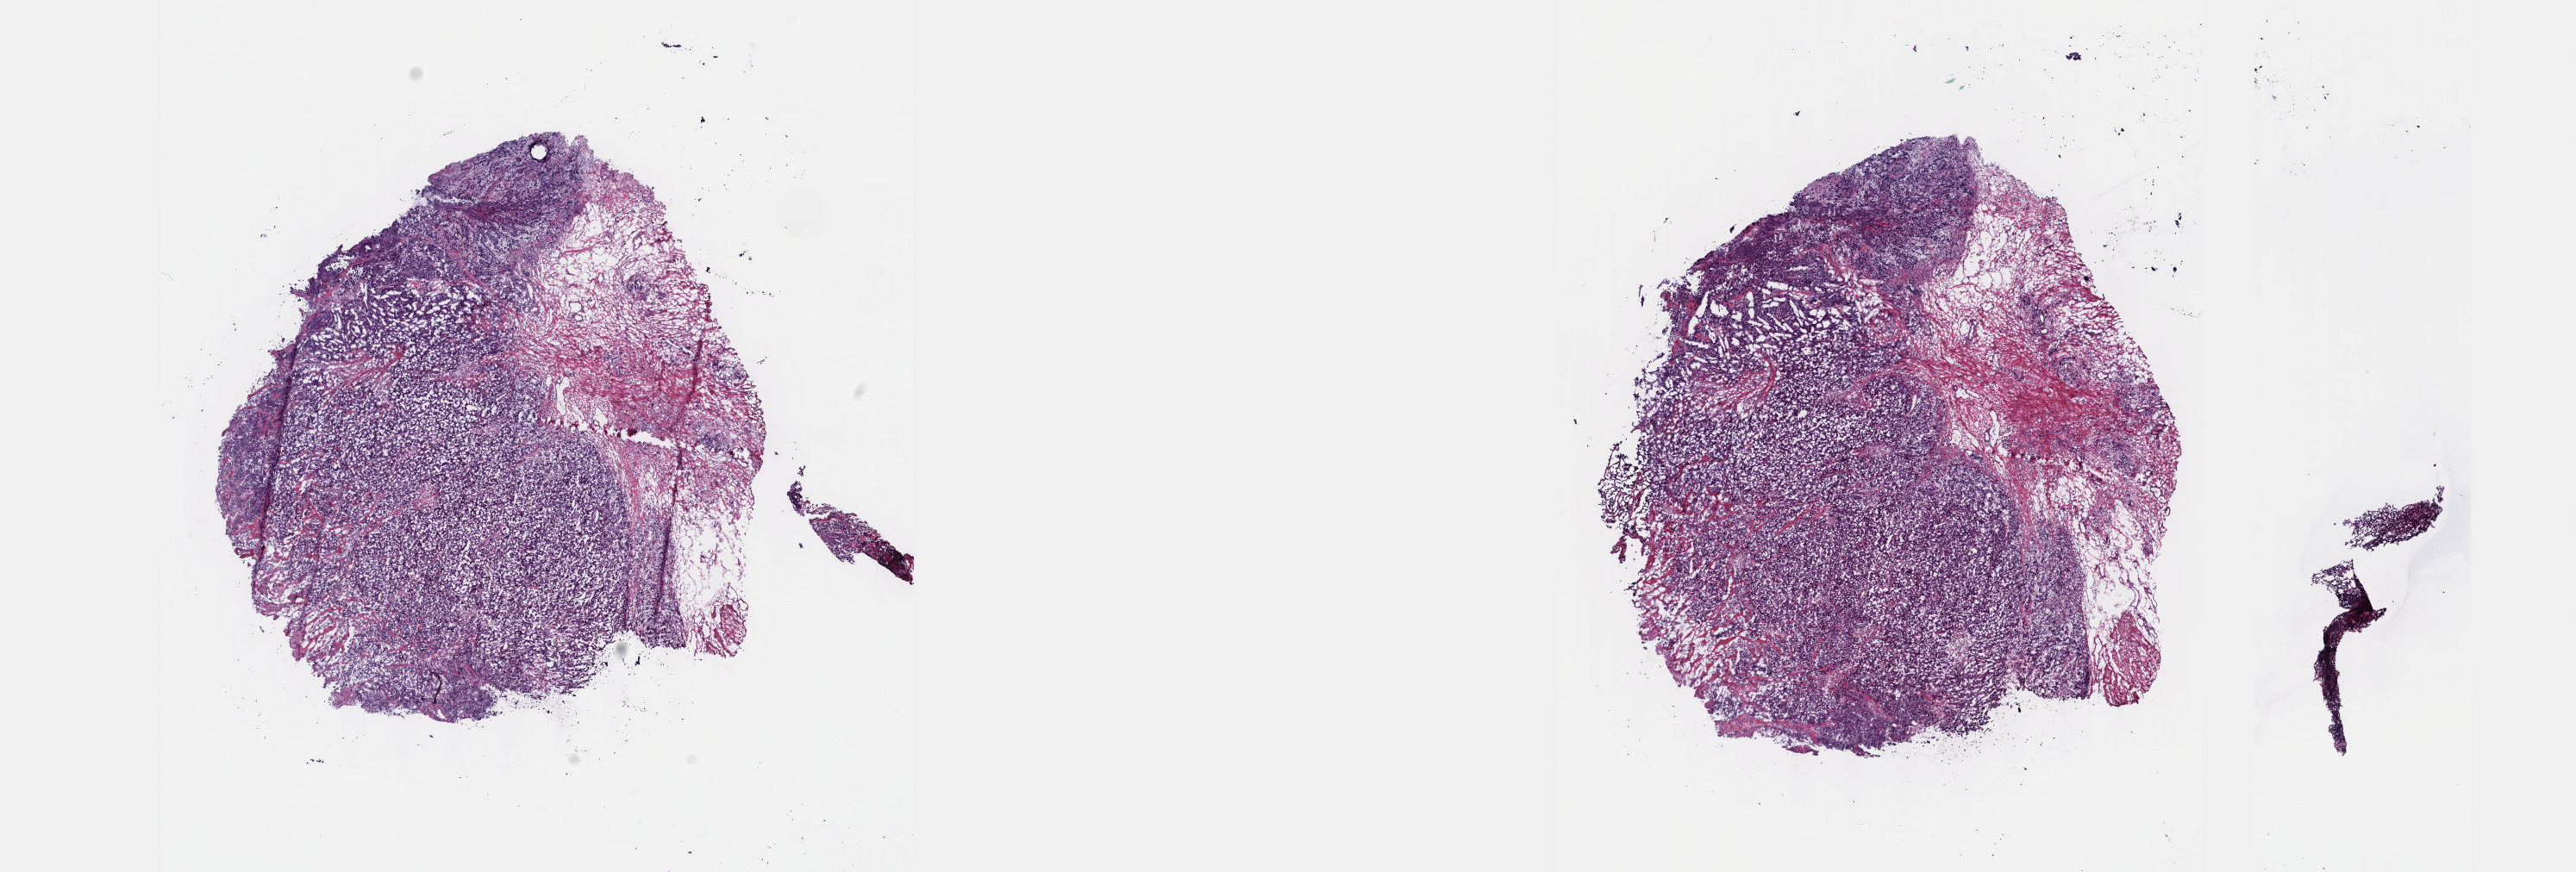
Hematoxylin and eosin (H&E) stained whole-slide image — shown as a low-resolution overview of the whole scanned area (about 24.1 x 8.2 mm, slide scanned at 40x), frozen section from the top of the tissue portion, esophagus, primary tumour sample. Male, age 80 years at initial diagnosis. Histologic grade: G3 (poorly differentiated). Slide review estimates, as recorded: tumour cells 85%, tumour nuclei 70%, normal cells 15%, stromal cells 0%, necrosis 0%. Inflammatory infiltration, as recorded: lymphocyte infiltration 5%, monocyte infiltration 0%, neutrophil infiltration 0%.
Lymph nodes positive (case pathology): 2 of 14 examined. AJCC pathologic stage: III. TNM: T3 N1 M0. Histologic diagnosis: Adenocarcinoma, NOS (lower third of esophagus).